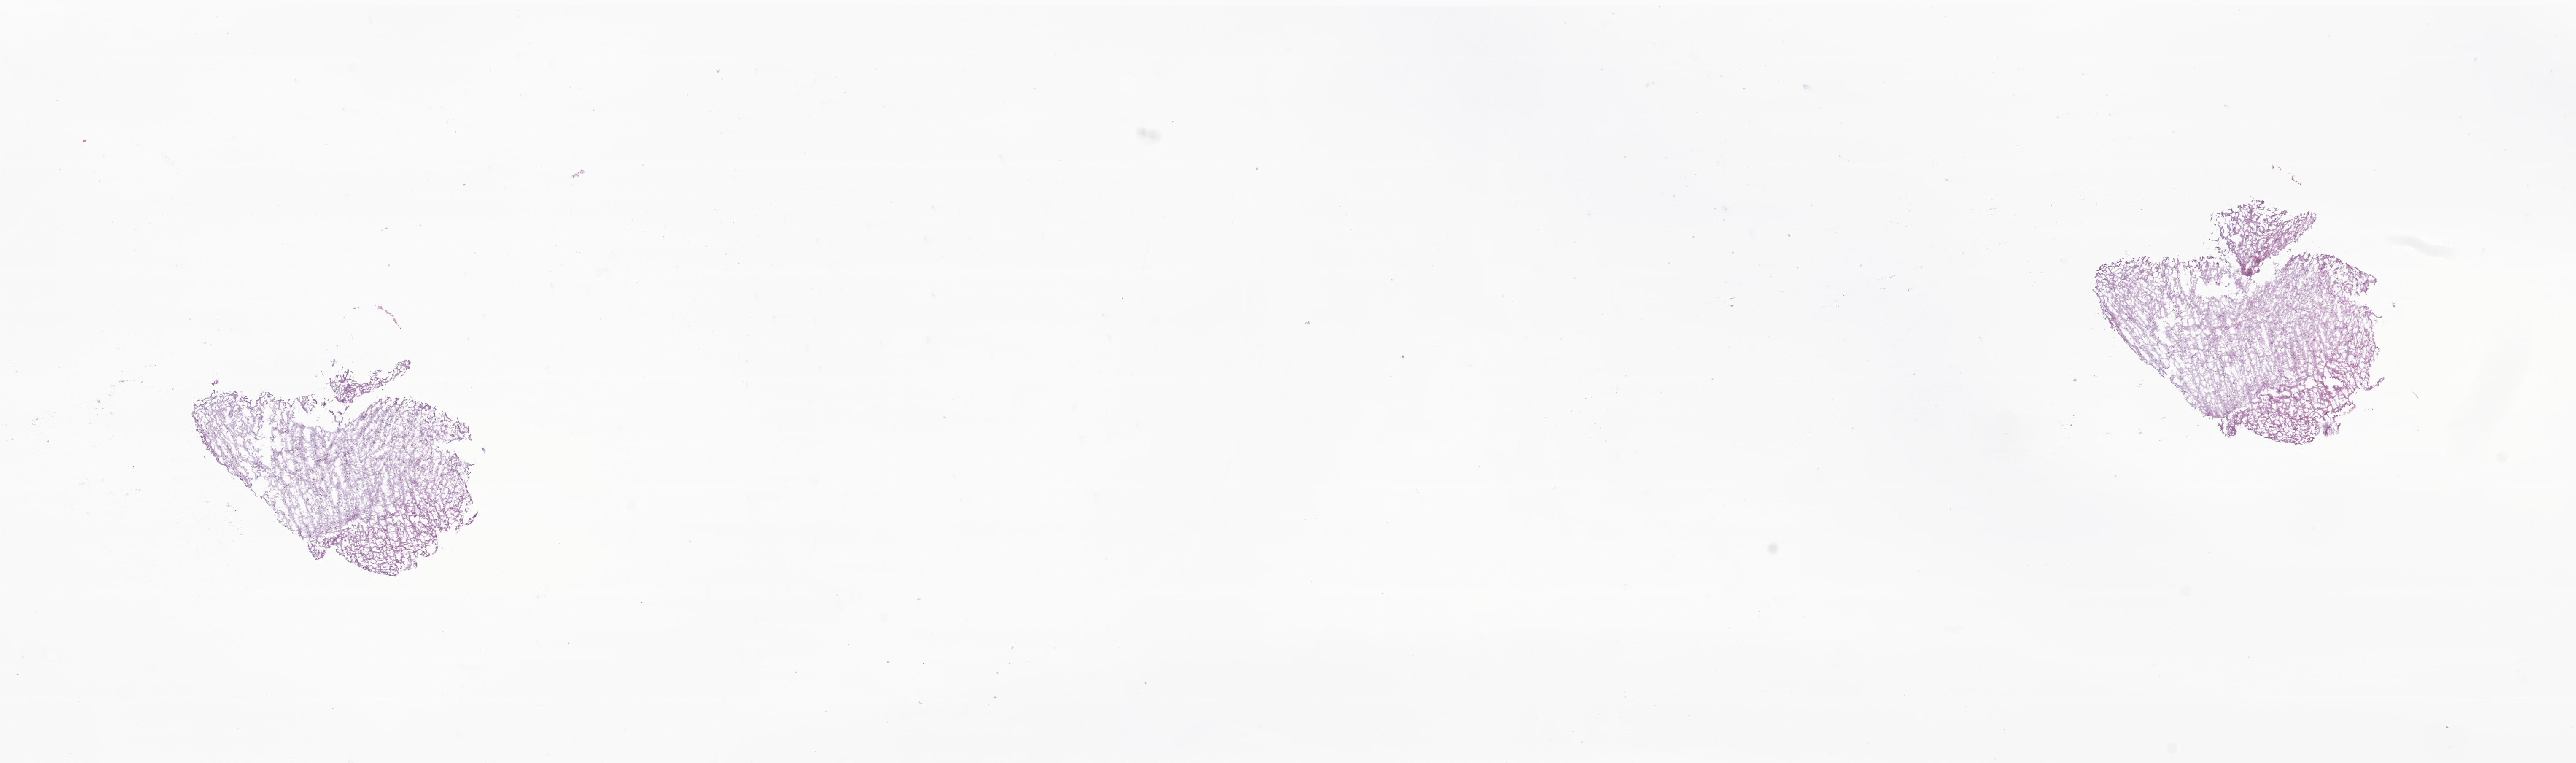
Whole-slide image, haematoxylin and eosin stain of tumor tissue from the brain, shown as a low-resolution overview of the whole scanned area (about 25.8 x 7.6 mm). Frozen section (OCT-embedded). Patient female; age 119 months (9 years 11 months).
* diagnosis: Glioma, malignant